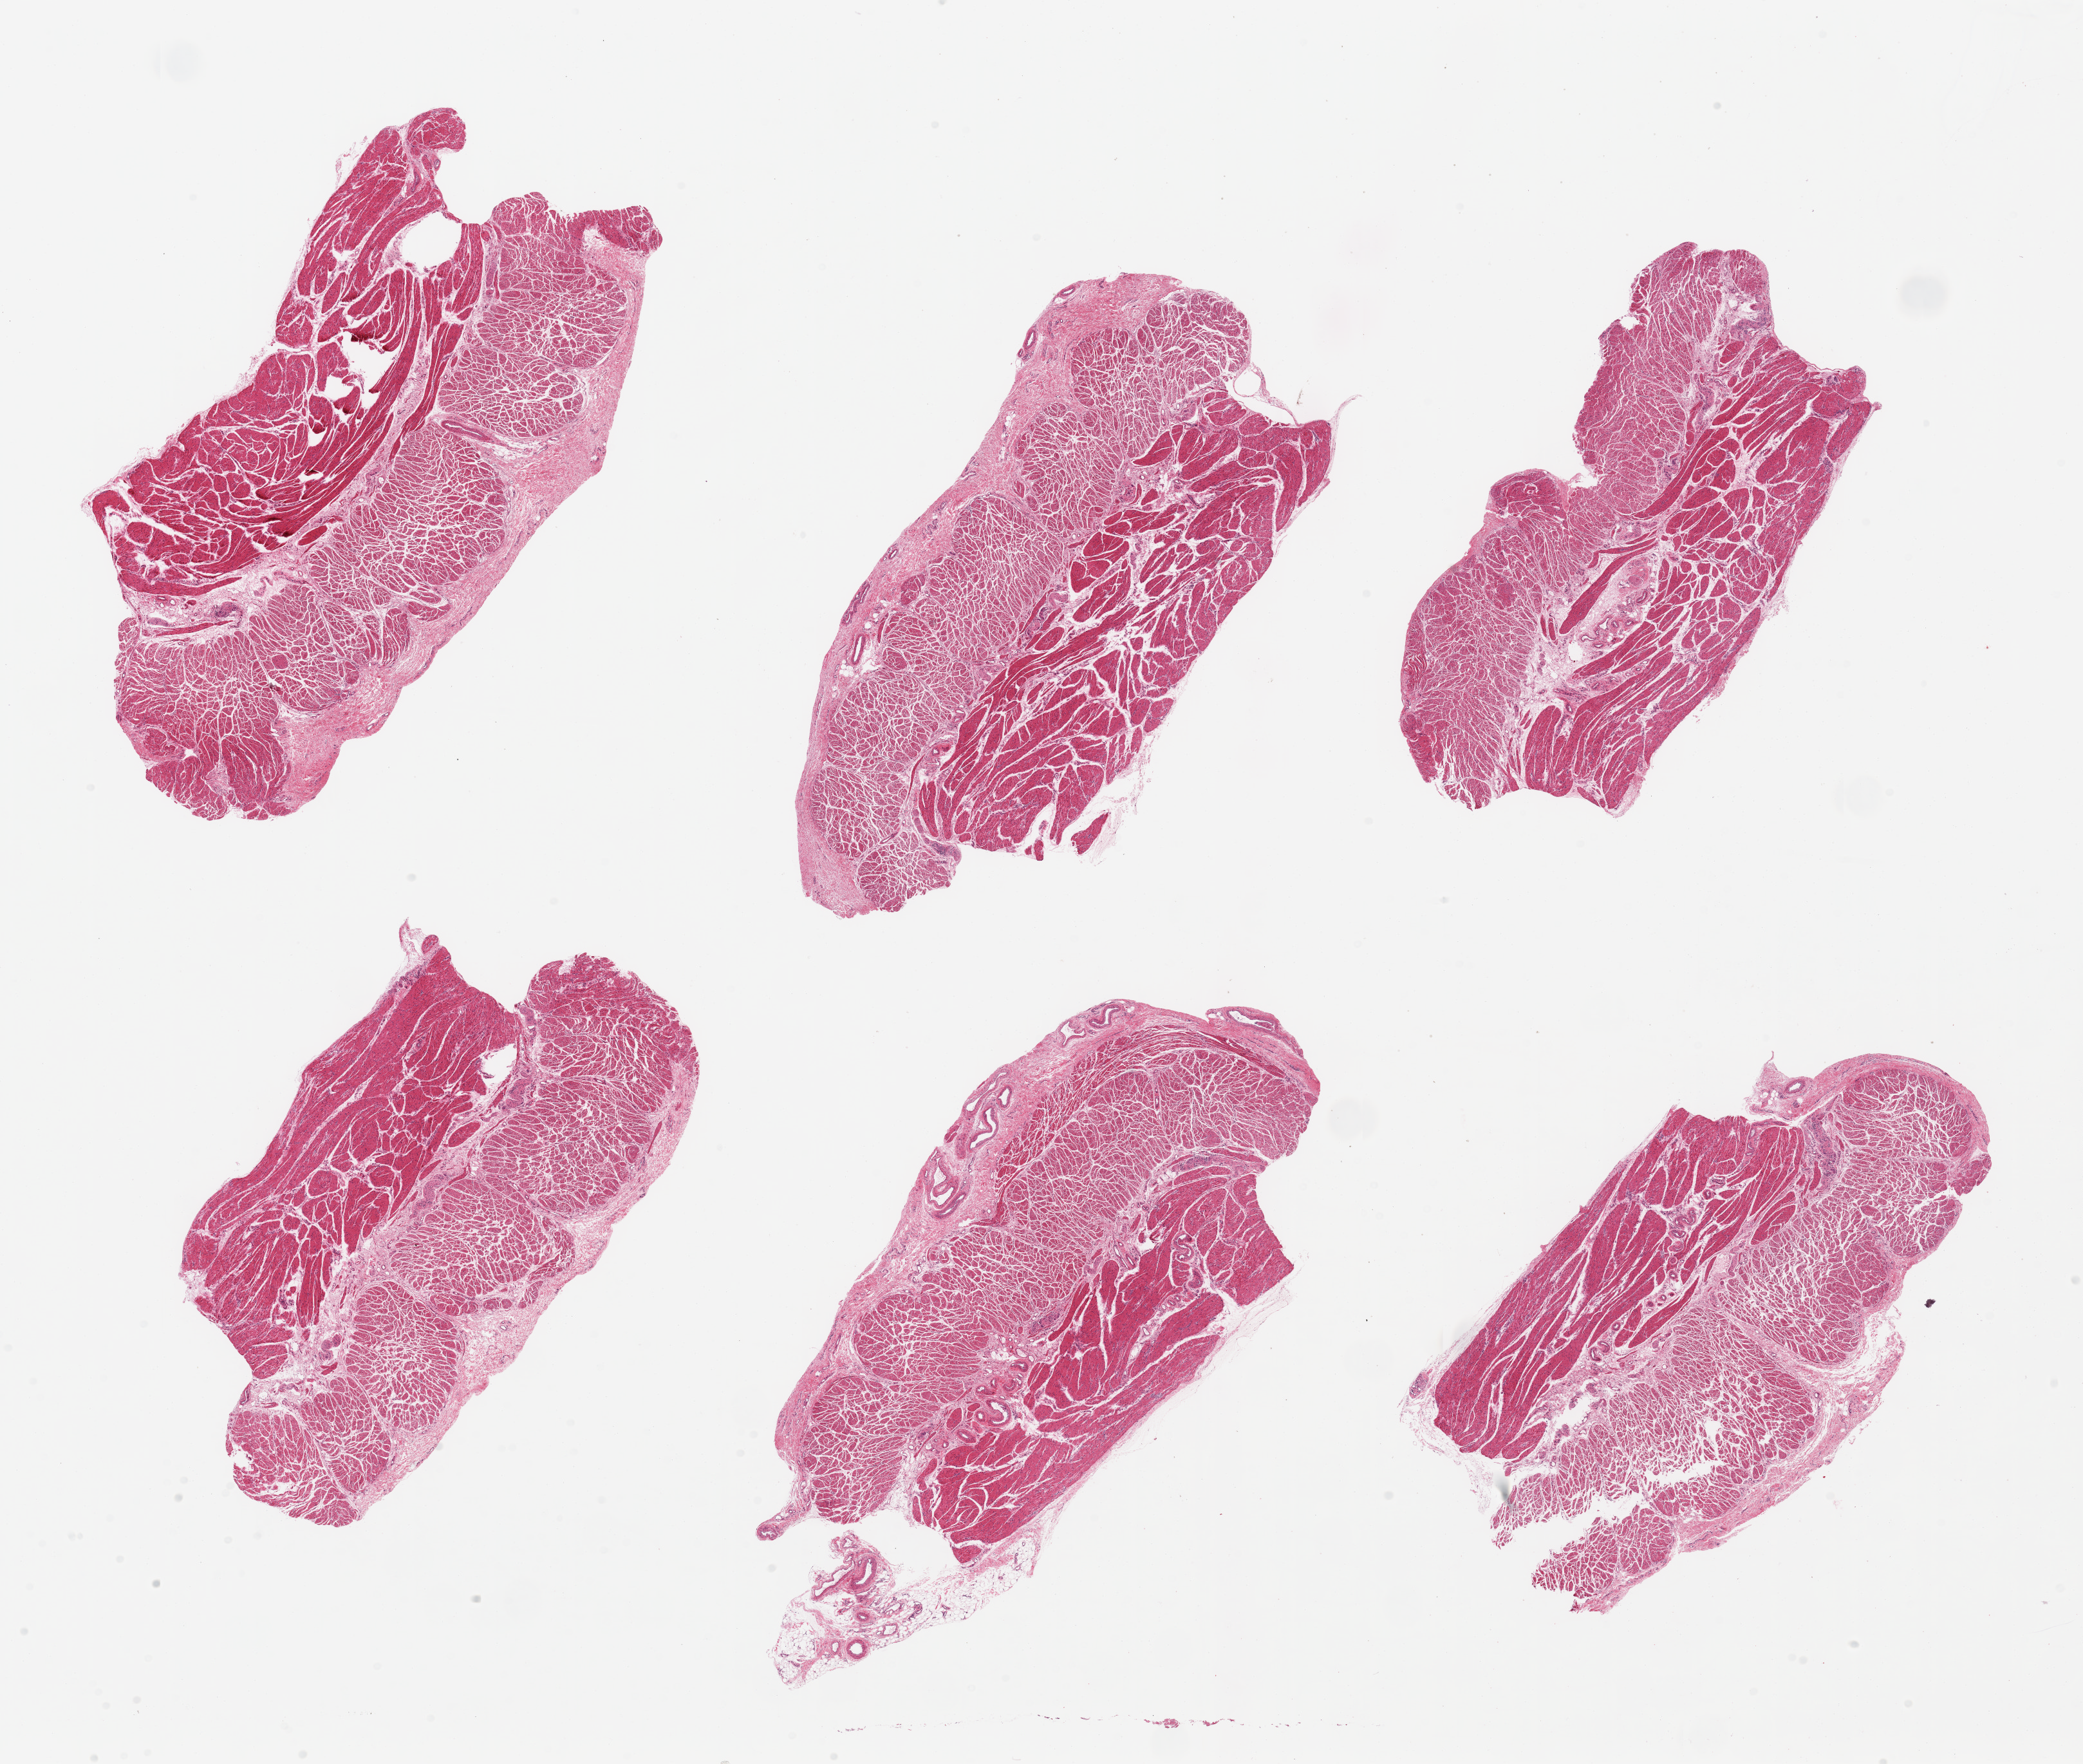
Haematoxylin and eosin whole-slide image, a low-resolution overview of the entire scanned area, about 25.6 x 21.7 mm; PAXgene-fixed, paraffin-embedded tissue; section of esophageal muscle (target tissue); donor tissue sample. Donor: male.
Pathologist's review note for this sample: 6 pieces, confirmed target muscularis.